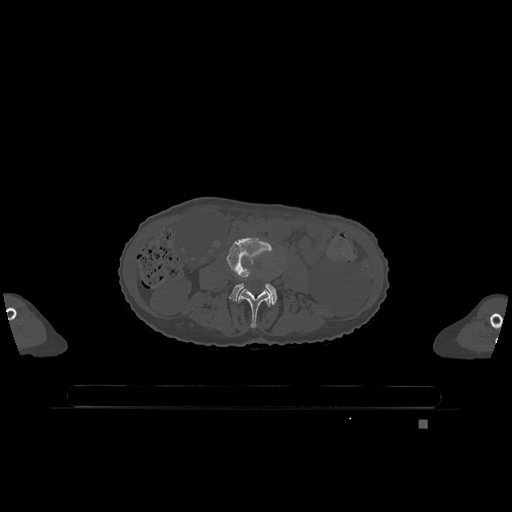
CT including the spine, one axial slice. Position 333 of 1317 along the scan axis. Bone window (W 1800 / L 400 HU). 512 × 512 image matrix, field of view 500 × 500 mm. Female patient, age 74 years. From the clinical record (not read from this slice): primary cancer: lung.
Annotated regions visible in this slice (semi-automatically segmented with operator editing):
- L3 vertebra: bounding box [x1, y1, x2, y2] px = [238, 289, 273, 328]
- L4 vertebra: [227, 238, 277, 305]